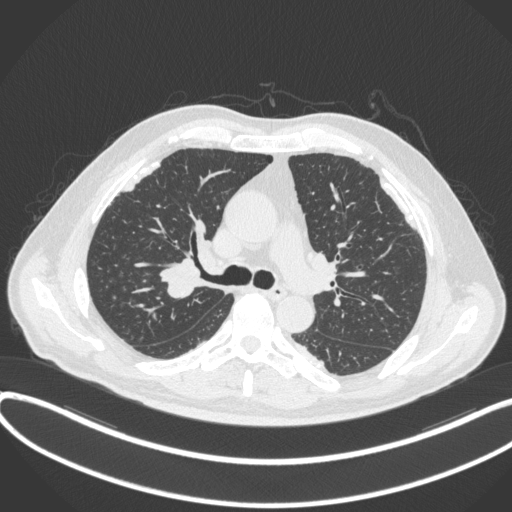
Chest CT, one axial slice; slice 273 of 455 in the series (ordered by position); reconstruction kernel B31f; lung window (W 1500 / L -600 HU); 1 mm slice thickness; 512 × 512 image matrix, field of view 400 × 400 mm. Male patient, age 58 years. Case-level facts recorded for this patient, not image findings: clinical TNM (as recorded): T1c N0 M0.
Structures marked on this image (bounding box drawn by a radiologist):
- lung tumour (recorded histology: squamous cell carcinoma): bounding box (x1, y1, x2, y2) in pixels: (160, 259, 205, 303)